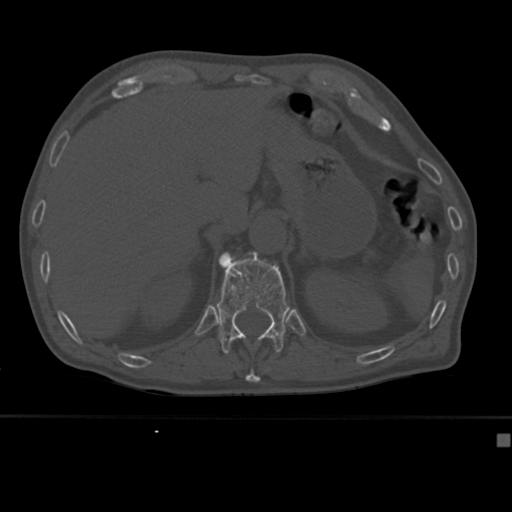
CT including the spine, one axial slice. Position 194 of 430 along the scan axis. 120 kVp. Bone window (W 1800 / L 400 HU). 1.5 mm slice thickness. 512 × 512 image matrix, field of view 337 × 337 mm. Male patient, age 64 years. Case-level facts recorded for this patient, not image findings: primary cancer: uterus; vertebrae with lytic lesions (as recorded): T1, T4, T5, T7, L5.
Annotated regions visible in this slice (semi-automatic segmentation, software-assisted and operator-edited):
- T11 vertebra: box from (x=245, y=369) to (x=261, y=382) px
- T12 vertebra: (x=216, y=252)–(x=290, y=354)